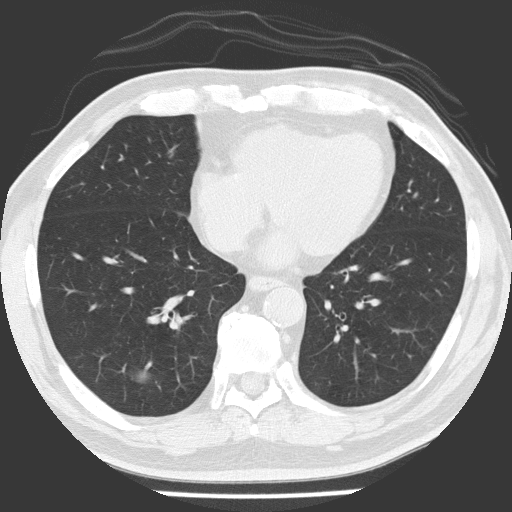
Chest CT (low-dose screening protocol), one axial image. Baseline screening round. Lung window (W 1500 / L -600 HU). 2 mm slice thickness. Lung (sharp) reconstruction kernel (FC51). 120 kVp. Male participant, aged 56 years at enrolment. Former smoker at enrolment.
Lesion marked by an expert reader, box from (x=105, y=342) to (x=164, y=405) px. Reader record for this screening exam (exam-level; its link to the box is not recorded): non-calcified nodule or mass ≥4 mm, right lower lobe, 21 × 17 mm, spiculated (stellate) margins, soft tissue attenuation. Official screen result: positive, change unspecified: nodule(s) >= 4 mm or enlarging nodule(s), mass(es), or other non-specific abnormalities suspicious for lung cancer. Lung cancer was diagnosed 84 days after this screen: adenocarcinoma, NOS, right lower lobe, poorly differentiated (G3), stage IA (AJCC 6th edition), 24 mm at pathology.